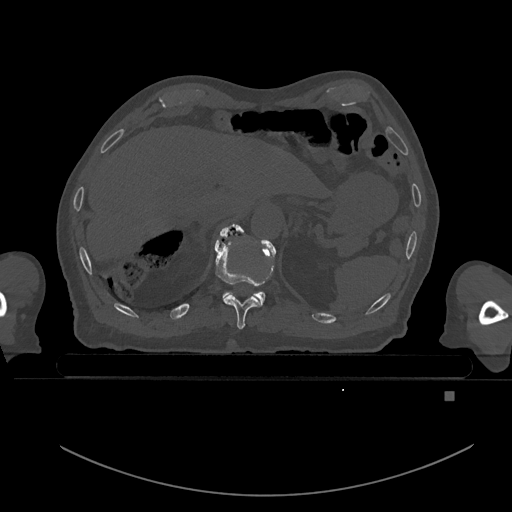
CT including the spine, one axial slice; slice 67 of 969 in the series (ordered by position); bone window (W 1800 / L 400 HU); 0.5 mm slice thickness; 512 × 512 image matrix, field of view 456 × 456 mm. Male patient, age 82 years. From the clinical record (not read from this slice): primary cancer: prostate.
Outlined on this slice (semi-automatically segmented with operator editing):
- T10 vertebra: box from (x=214, y=224) to (x=264, y=330) px
- T11 vertebra: (x=219, y=223)–(x=273, y=305)